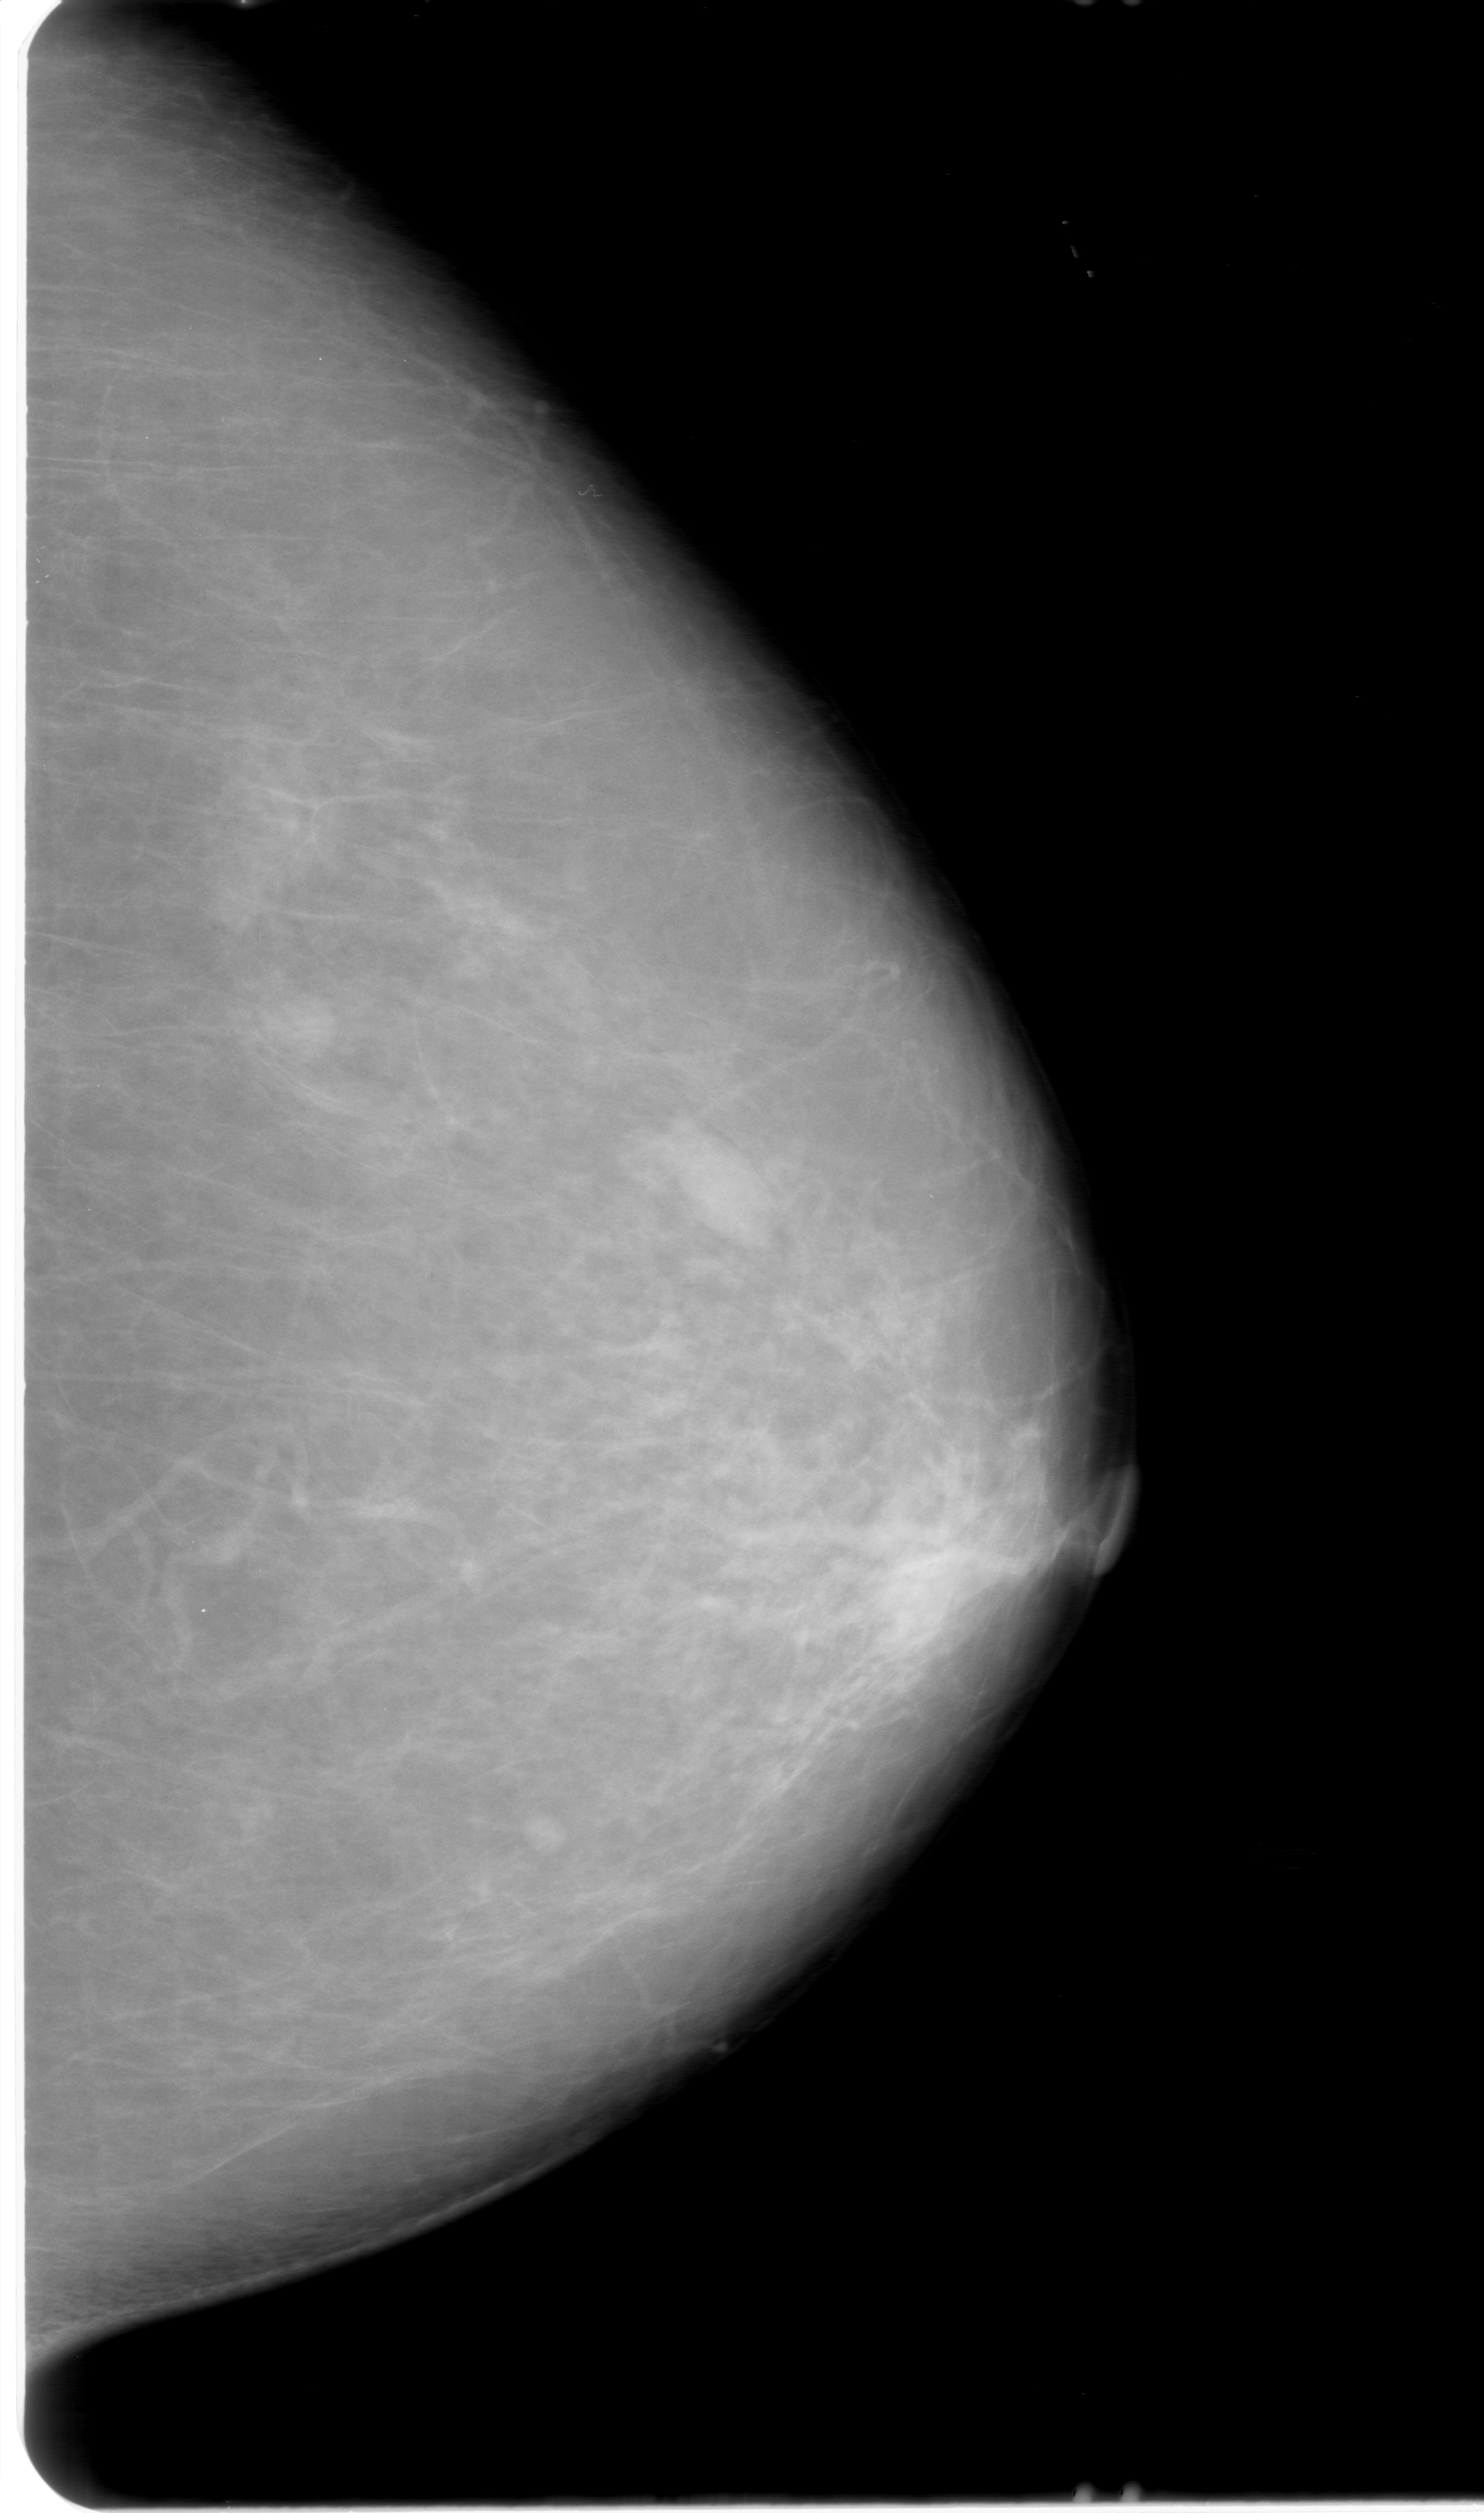
Scanned film-screen mammogram, left breast, craniocaudal (CC) view, breast composition: almost entirely fatty (BI-RADS density category 1 of 4).
Radiologist-marked abnormalities on this image: mass, shape oval, margins obscured; BI-RADS assessment category 0 (incomplete: needs additional imaging); subtlety rating 5 on a 1 (subtle) to 5 (obvious) scale; pathology (as recorded): benign.